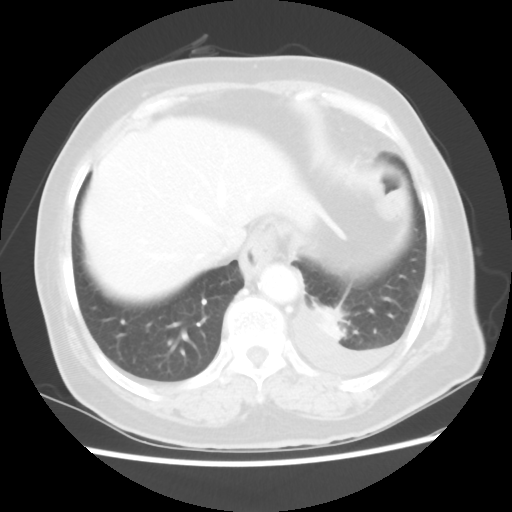
Chest CT, one axial slice. Position 10 of 80 along the scan axis. Reconstruction kernel STANDARD. 100 kVp. Lung window (W 1500 / L -600 HU). 5 mm slice thickness. 512 × 512 image matrix, field of view 343 × 343 mm. Patient: female, 68 years. Case-level facts recorded for this patient, not image findings: clinical TNM (as recorded): T1c N0 M1.
Annotated regions visible in this slice (rectangle marked by the reading radiologist):
- lung tumour (recorded histology: adenocarcinoma): bounding box [x1, y1, x2, y2] px = [311, 299, 358, 341]